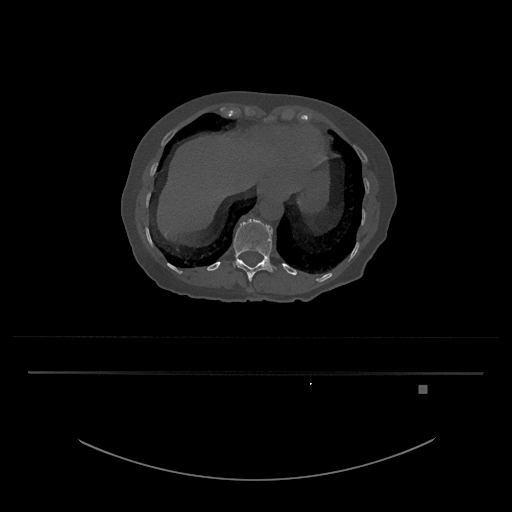
CT including the spine, one axial slice; position 611 of 797 along the scan axis; bone window (W 1800 / L 400 HU); 0.5 mm slice thickness; 512 × 512 image matrix, field of view 500 × 500 mm. Patient: female, 57 years. From the clinical record (not read from this slice): primary cancer: cervical.
Structures marked on this image (semi-automatically segmented with operator editing):
- T12 vertebra: bounding box [x1, y1, x2, y2] px = [233, 219, 276, 282]